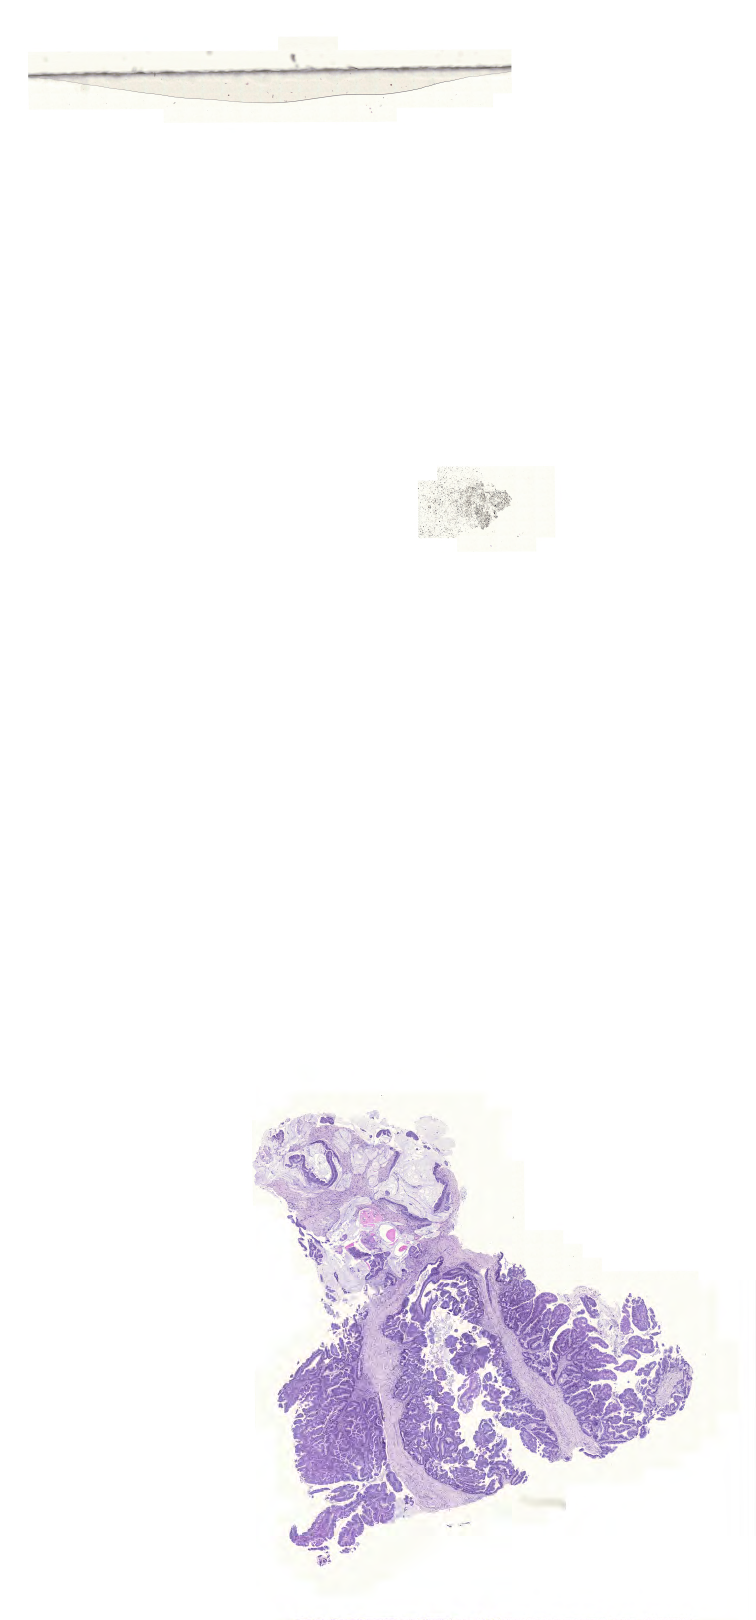
Hematoxylin and eosin (H&E) stained whole-slide image — a low-resolution overview of the entire scanned area, about 11.2 x 24.1 mm, formalin-fixed paraffin-embedded (FFPE) diagnostic section, primary tumour sample from the colon. Male, age 69 years at initial diagnosis.
Histologic diagnosis: Mucinous adenocarcinoma. Lymph nodes positive (case pathology): 2 of 24 examined. AJCC pathologic stage: IIIB.